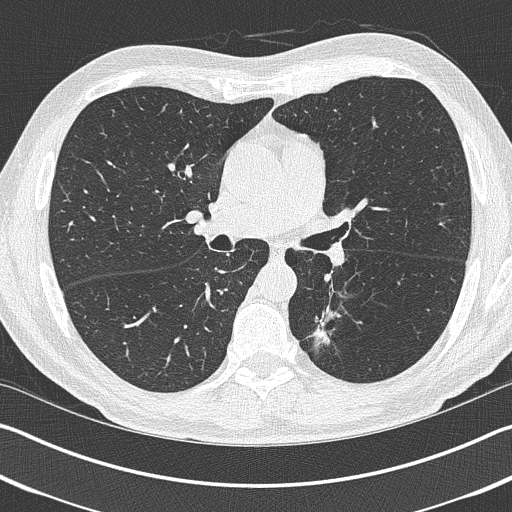
Axial slice from a low-dose chest CT screening exam, baseline annual screen, lung window (W 1500 / L -600 HU), lung (sharp) reconstruction kernel (B50f), slice 164 of 402 in the series. Male, age 69 years at enrolment.
Lesion marked by an expert reader, bounding box (x1, y1, x2, y2) in pixels: (299, 307, 354, 361). The exam's reader record, not a measurement of the box and not confirmed to be the same lesion: non-calcified nodule or mass ≥4 mm, left upper lobe, 19 × 19 mm, spiculated (stellate) margins, pre-existing on the prior screen: yes. Official screen result: positive, change unspecified: nodule(s) >= 4 mm or enlarging nodule(s), mass(es), or other non-specific abnormalities suspicious for lung cancer. Lung cancer was diagnosed 202 days after this screen: non-small cell carcinoma, left lower lobe, stage IIIA (AJCC 6th edition), 20 mm at pathology.